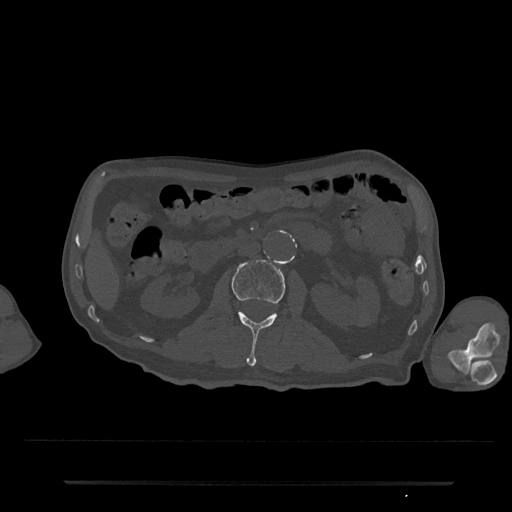
CT including the spine, one axial slice. Position 53 of 797 along the scan axis. Reconstruction kernel Br40s/3. 120 kVp. Bone window (W 1800 / L 400 HU). 0.5 mm slice thickness. 512 × 512 image matrix. Male patient, age 74 years. From the clinical record (not read from this slice): primary cancer: prostate.
Structures marked on this image (semi-automatic segmentation, software-assisted and operator-edited):
- L2 vertebra: box from (x=232, y=259) to (x=285, y=366) px